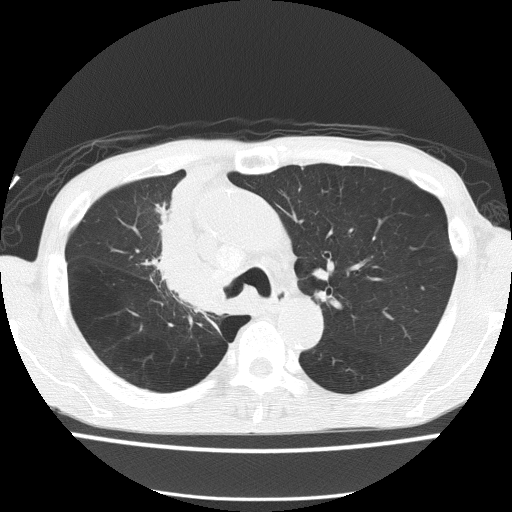
Low-dose screening chest CT, one axial slice; position 102 of 150 along the scan axis; 120 kVp; lung window (W 1500 / L -600 HU); 2 mm slice thickness; 512 × 512 image matrix, field of view 336 × 336 mm.
Outlined on this slice (outlined manually by an expert reader):
- lesion 1 (tumor, hilum of right lung): bounding box <161,173,226,311> (left, top, right, bottom; pixels)